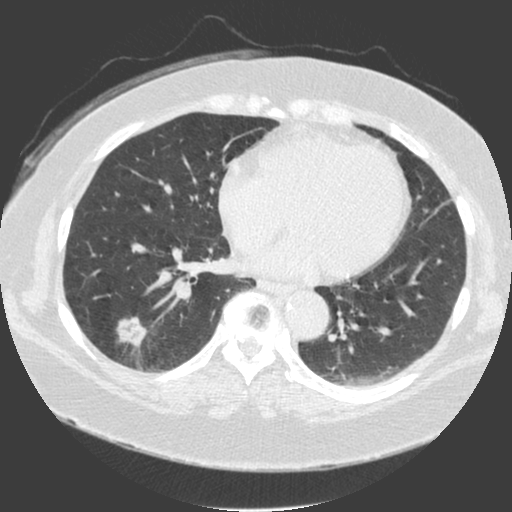
Low-dose screening chest CT, one axial slice. Lung window (W 1500 / L -600 HU). 2 mm slice thickness. 512 × 512 image matrix, field of view 370 × 370 mm.
Structures marked on this image (expert manual segmentation):
- lesion 1 (tumor, lower lobe of right lung): box from (x=117, y=317) to (x=147, y=347) px